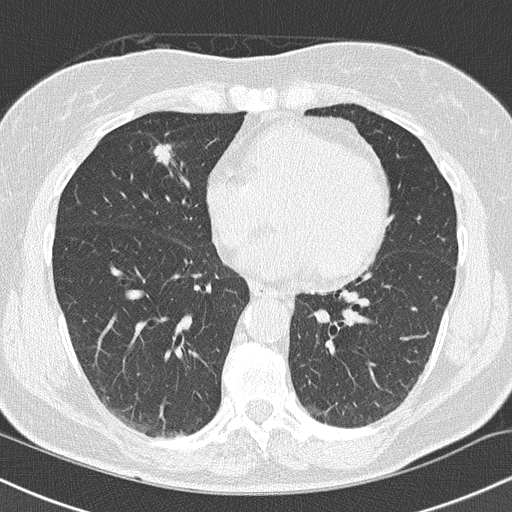
Axial slice from a low-dose chest CT screening exam, baseline screening round, lung window (W 1500 / L -600 HU), slice 85 of 145 in the series. Female, age 66 years at enrolment. Current smoker at enrolment.
- Expert reader's lesion annotation, bounding box <145,133,177,166> (left, top, right, bottom; pixels).
- Reader record for this screening exam (exam-level; its link to the box is not recorded): non-calcified nodule or mass ≥4 mm, right lower lobe, 10 × 8 mm, smooth margins, soft tissue attenuation.
- Participant outcome: lung cancer diagnosed 96 days after this screen — squamous cell carcinoma, keratinizing, NOS, right upper lobe, right middle lobe, poorly differentiated (G3), stage IA (AJCC 6th edition), 14 mm at pathology.